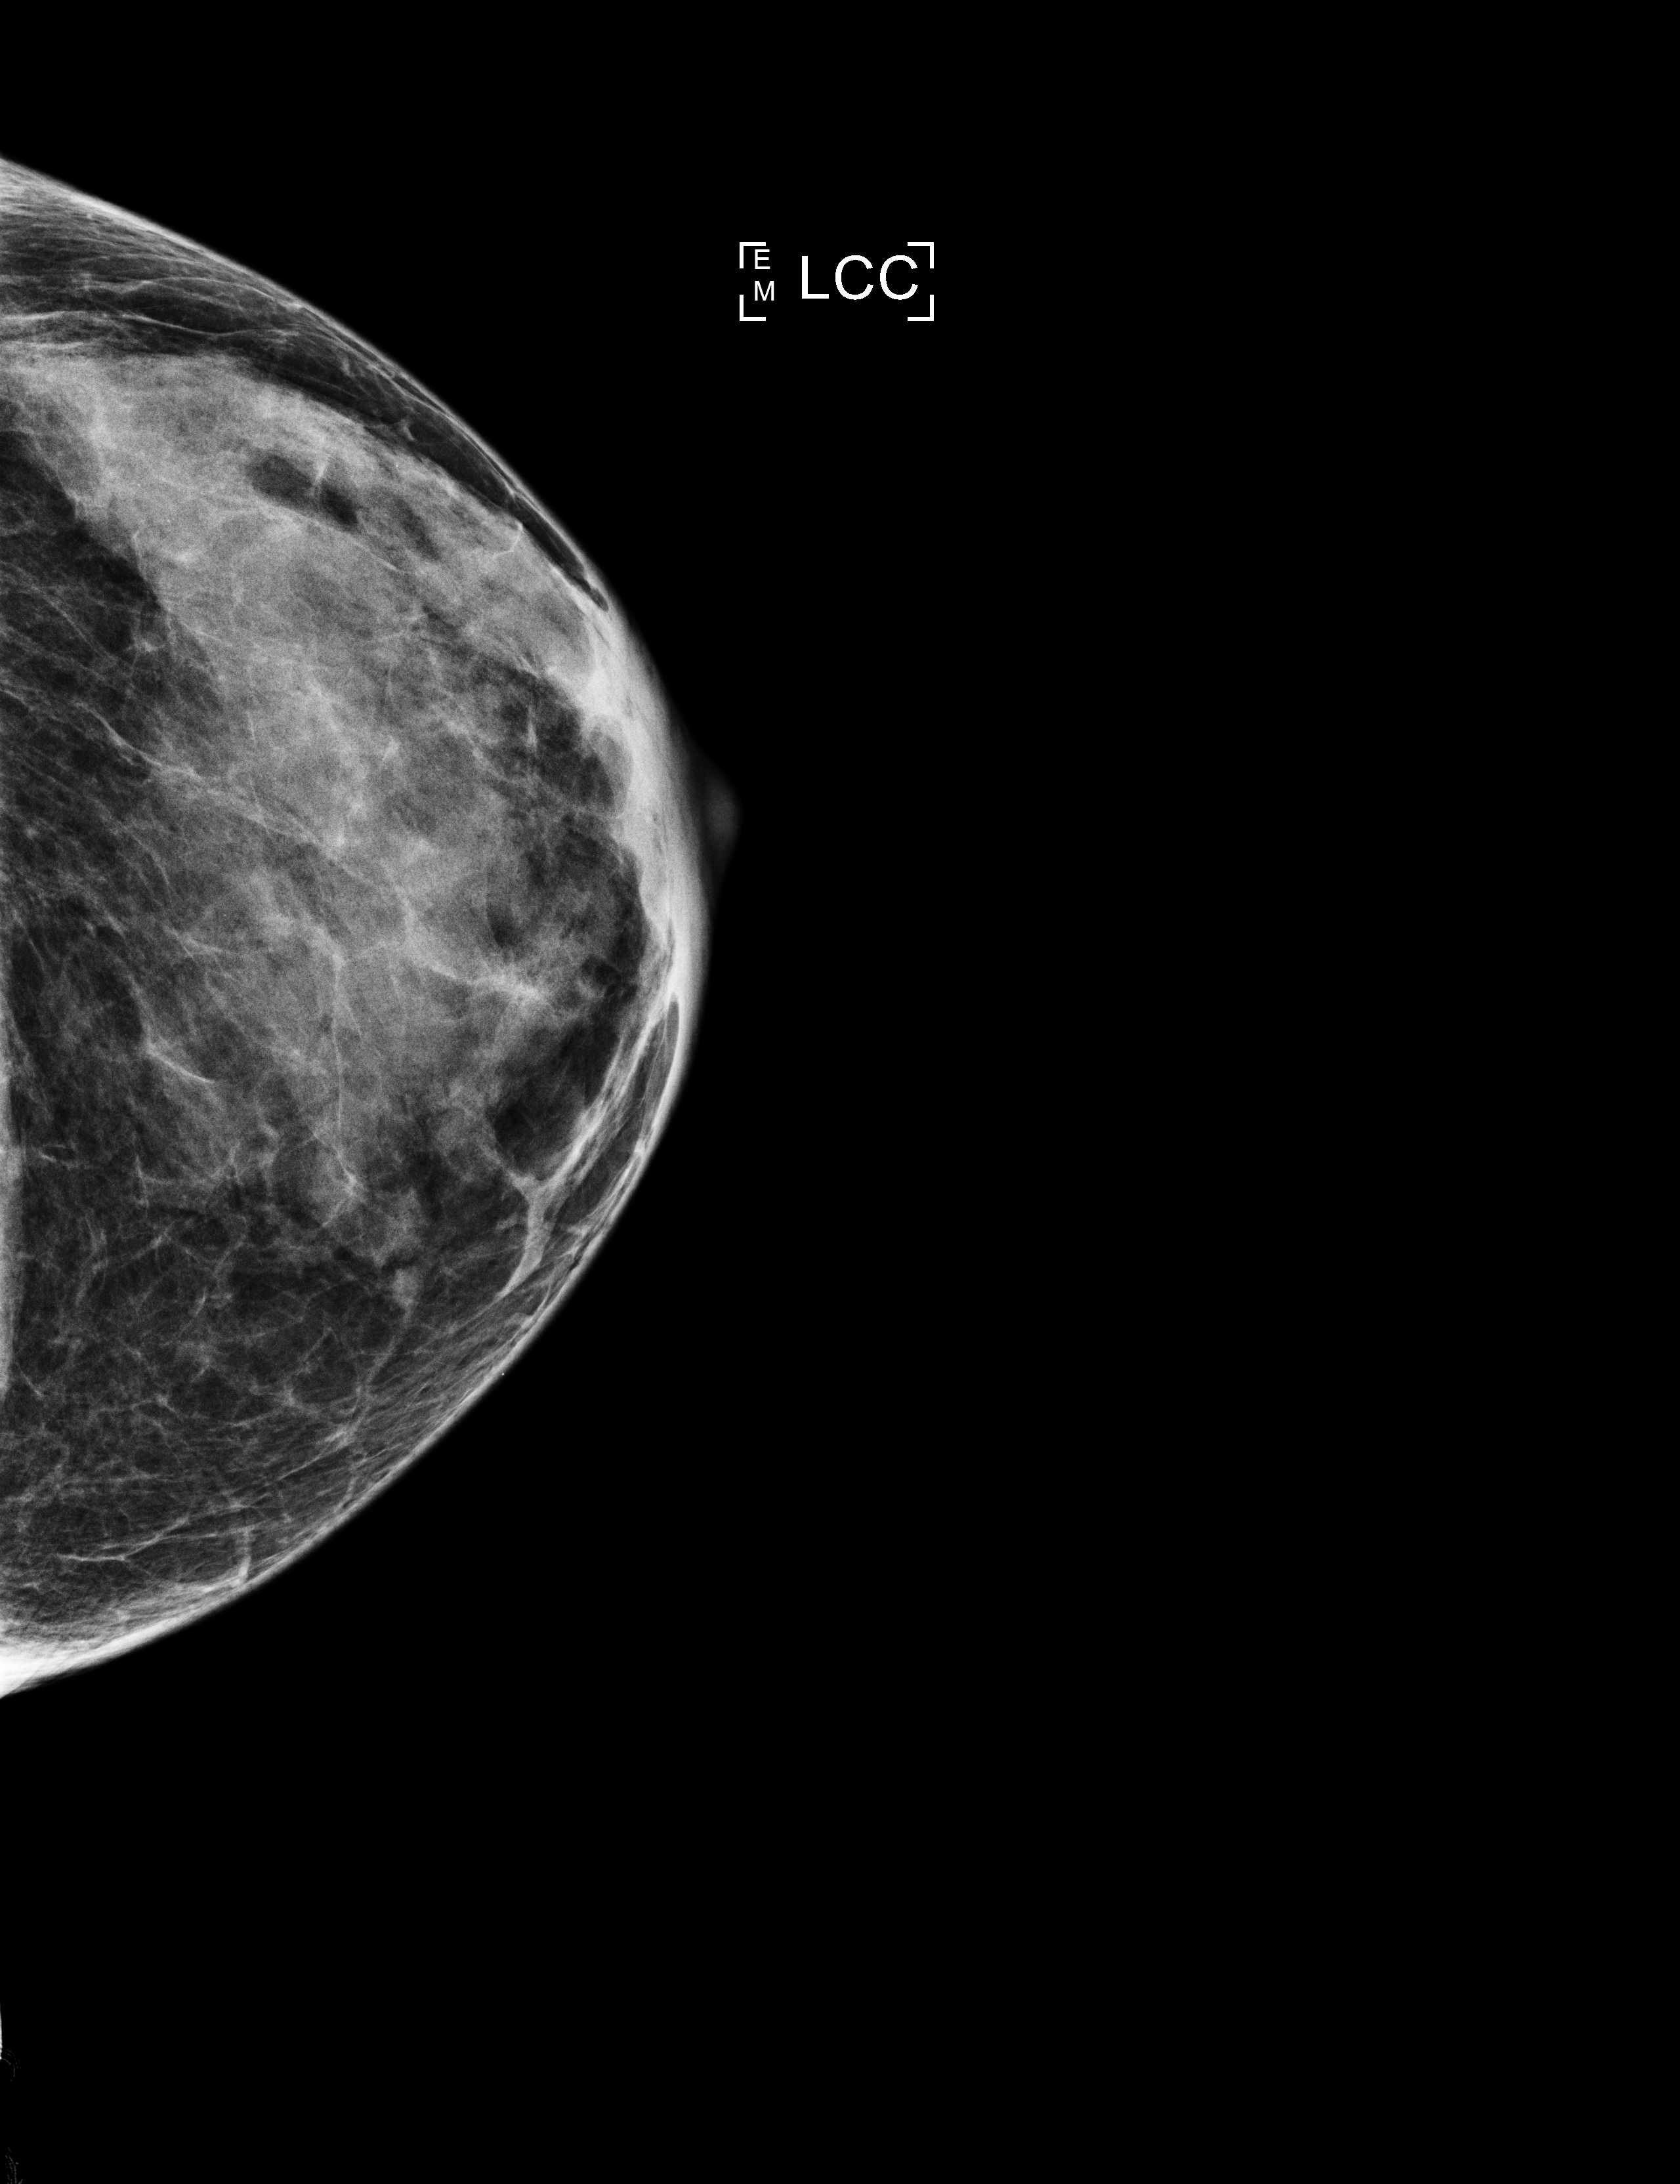
Full-field digital mammogram (FFDM), left breast, cranio-caudal projection, annual screening mammography examination. Female patient, age 65 years.
BI-RADS breast density category at the screening exam (both breasts, scale 1–4): 4. Final BI-RADS assessment for this screening round (tomosynthesis exam, both breasts): category 2. Recall: recalled for additional imaging after this screen.